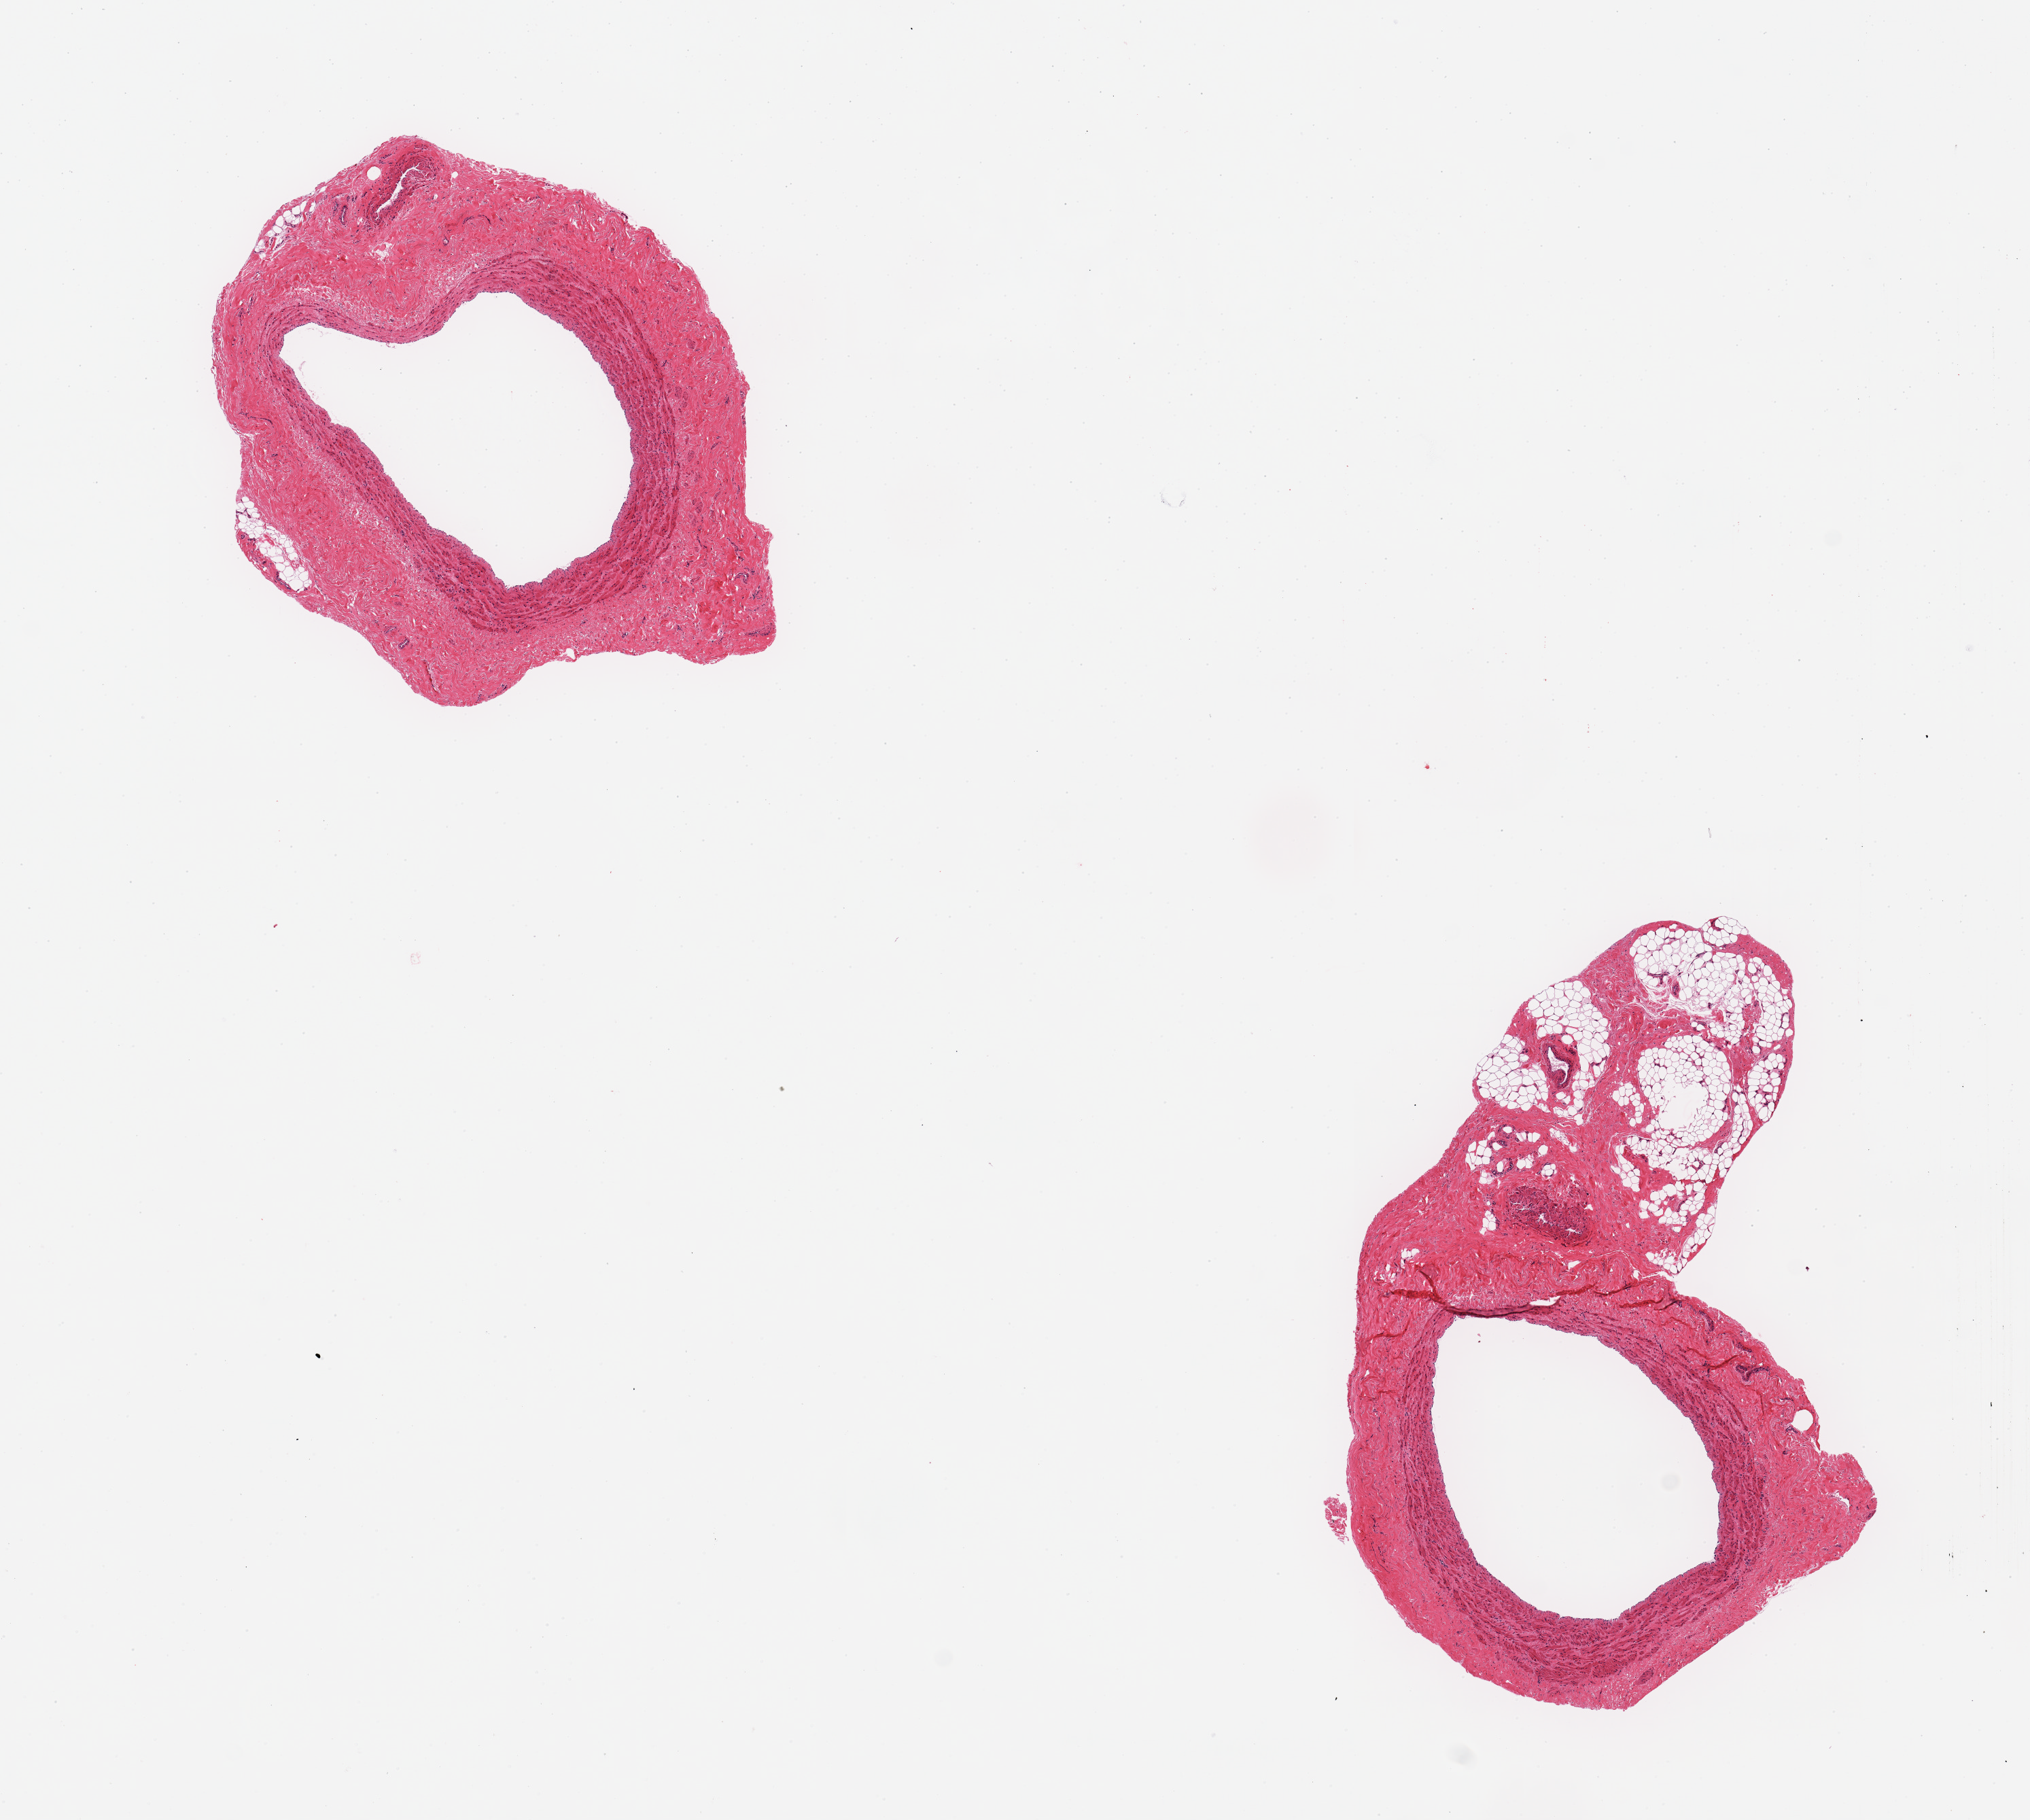
Whole-slide image, haematoxylin and eosin stain, brightfield, low-resolution overview of the scanned area, about 11.8 x 10.6 mm (acquisition: 20x scan), PAXgene-fixed, paraffin-embedded tissue, target tissue: tibial artery, donor tissue sample. Female donor.
• pathologist's review note for this sample: 2 pieces, ~30% of tissue is adherent fatty nubbin